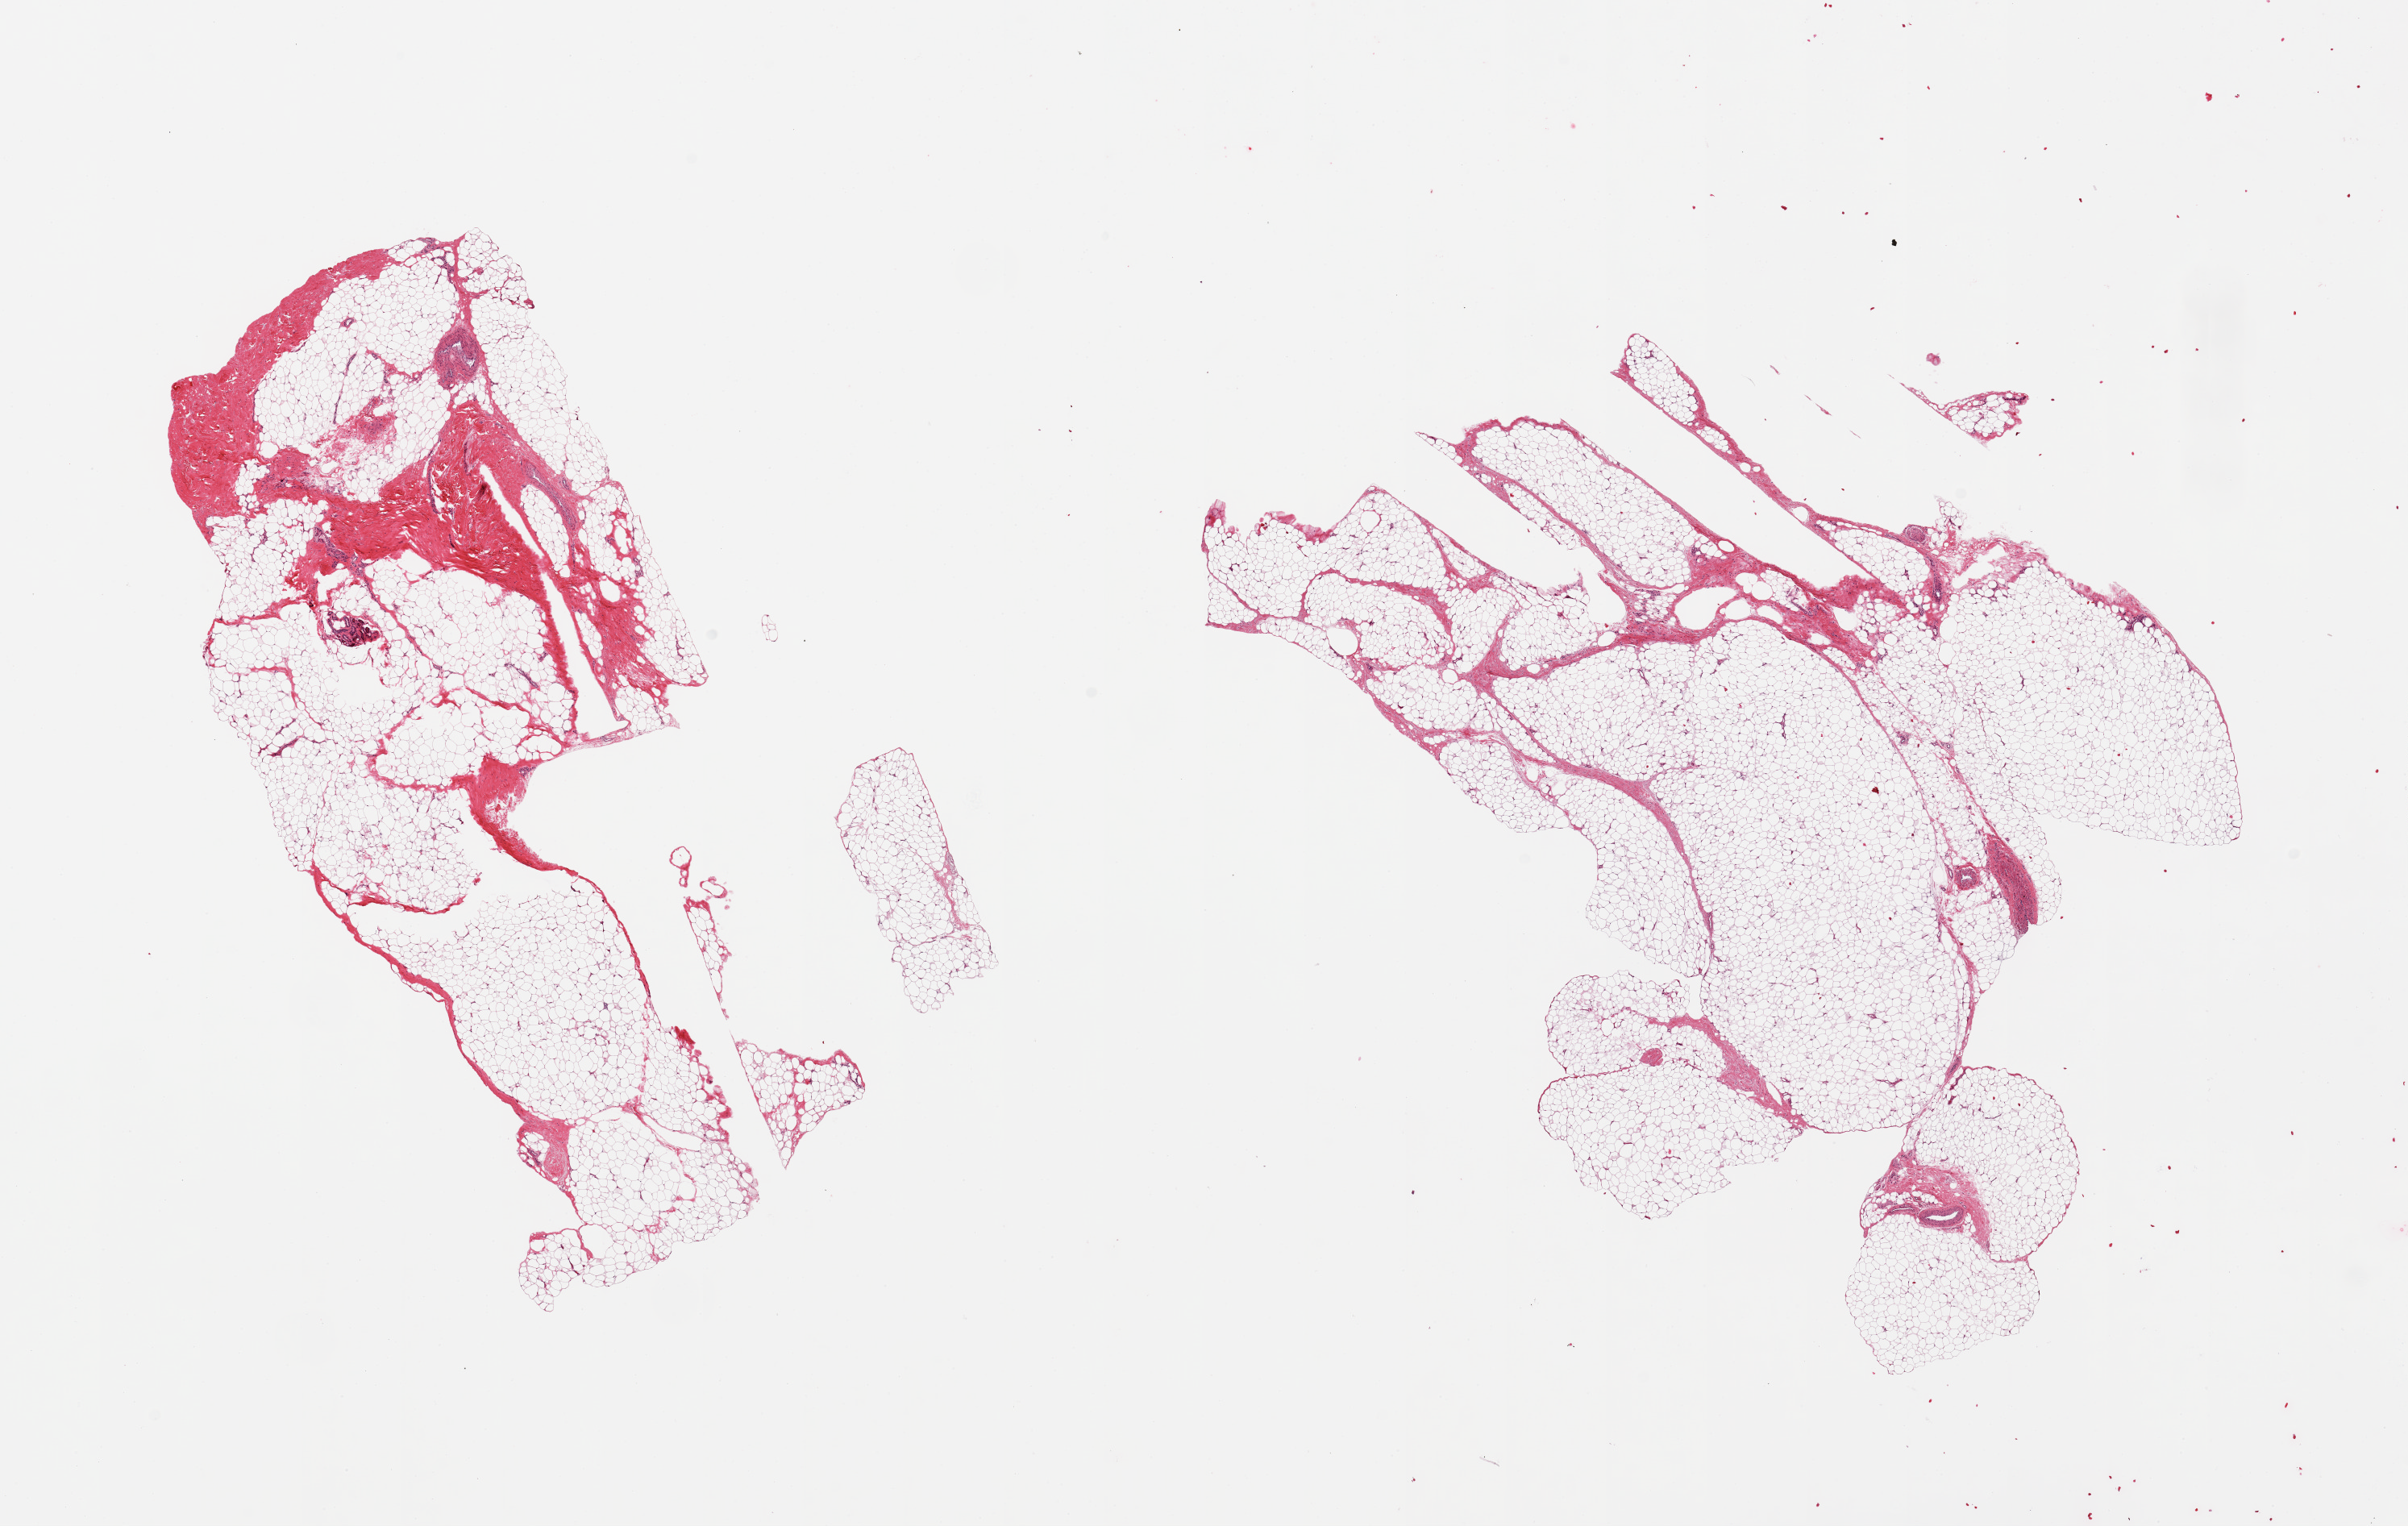
H&E whole-slide image — shown as a low-resolution overview of the whole scanned area (about 23.6 x 15.0 mm); PAXgene-fixed, paraffin-embedded tissue; section of adipose tissue (target tissue); tissue donor sample. Male donor.
Pathologist's review note for this sample: 2 pieces; ~15% of one and 5% of the second is fibrovascular tissue, few sweat glands.